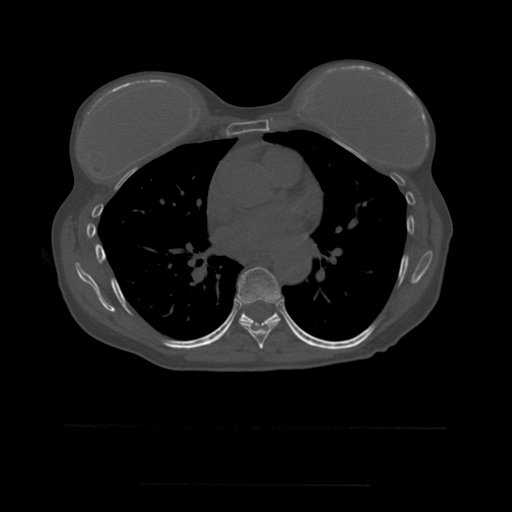
CT including the spine, one axial slice; position 350 of 544 along the scan axis; bone window (W 1800 / L 400 HU); 1.25 mm slice thickness; 512 × 512 image matrix, field of view 350 × 350 mm. Patient age 58 years. Case-level facts recorded for this patient, not image findings: primary cancer: lung.
Structures marked on this image (semi-automatically segmented with operator editing):
- T7 vertebra: bounding box (x1, y1, x2, y2) in pixels: (237, 267, 281, 349)
- T8 vertebra: (241, 303, 280, 330)